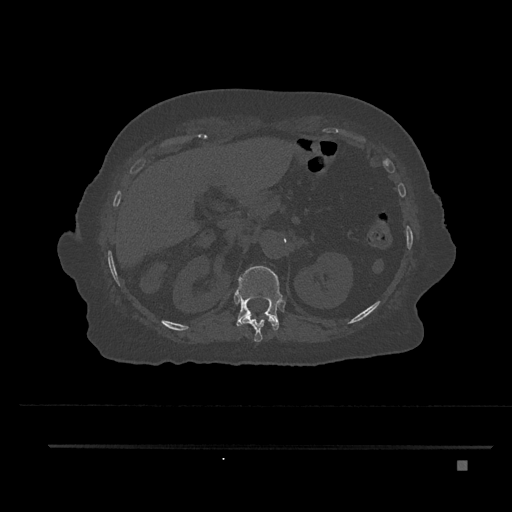
CT including the spine, one axial slice. Position 282 of 797 along the scan axis. Reconstruction kernel Br40s/3. Bone window (W 1800 / L 400 HU). 0.5 mm slice thickness. 512 × 512 image matrix, field of view 437 × 437 mm. Patient: female, 76 years. From the clinical record (not read from this slice): primary cancer: lung; vertebrae with lytic lesions (as recorded): T11, L3.
Outlined on this slice (semi-automatically segmented with operator editing):
- T11 vertebra: bounding box <241,314,275,342> (left, top, right, bottom; pixels)
- T12 vertebra: <236,266,283,332>